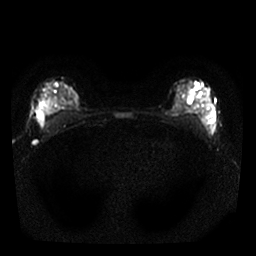
Breast MRI, one axial slice. Slice 18 of 25 in the series (ordered by position). Diffusion-weighted series; image 2 of 4 stored at this slice position (different b-values; order by instance number). 1.5 T. 4 mm slice thickness. 256 × 256 image matrix, field of view 290 × 290 mm. Female patient.
Outlined on this slice (outlined manually by an expert reader):
- tumour on diffusion-weighted imaging: bounding box (x1, y1, x2, y2) in pixels: (38, 97, 64, 130)